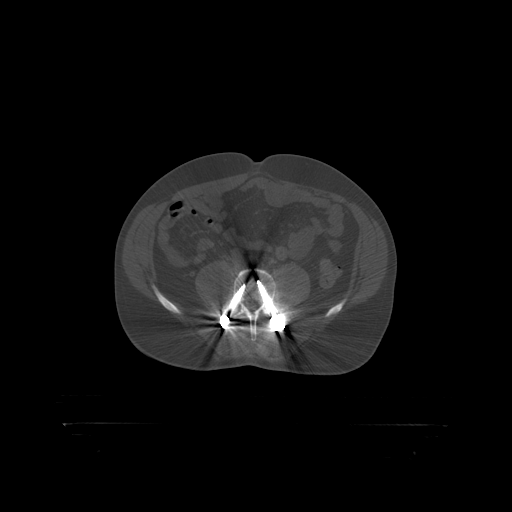
CT including the spine, one axial slice. Position 212 of 399 along the scan axis. Reconstruction kernel STANDARD. 120 kVp. Bone window (W 1800 / L 400 HU). 1.25 mm slice thickness. 512 × 512 image matrix, field of view 650 × 650 mm. Patient: male, 46 years. Case-level facts recorded for this patient, not image findings: primary cancer: skin.
Structures marked on this image (semi-automatic segmentation, software-assisted and operator-edited):
- L4 vertebra: bounding box (x1, y1, x2, y2) in pixels: (237, 314, 270, 317)
- L5 vertebra: (222, 270, 290, 319)